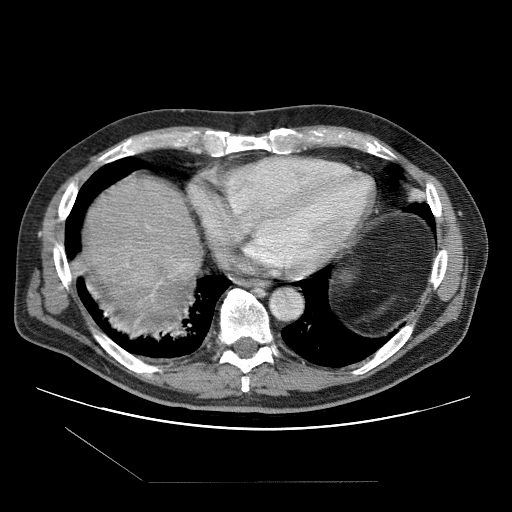
Contrast-enhanced abdominal CT (liver protocol), one axial slice; reconstruction kernel STANDARD; 120 kVp; one of 2 acquisitions stored at this slice position; soft-tissue window (W 400 / L 40 HU); 512 × 512 image matrix, field of view 400 × 400 mm. From the clinical record (not read from this slice): diagnosis: hepatocellular carcinoma (patient treated with transarterial chemoembolisation; whether this scan precedes or follows treatment is not stated here); TNM stage (as recorded): Stage-IIIB; Child-Pugh class: A; tumour differentiation: well differentiated.
Annotated regions visible in this slice (semi-automatic segmentation, software-assisted and operator-edited):
- liver parenchyma outside the tumour (the mass and vessels are separate outlines, so this box may not span the whole liver): box from (x=84, y=178) to (x=202, y=312) px
- liver vessels: (x=181, y=264)–(x=186, y=267)